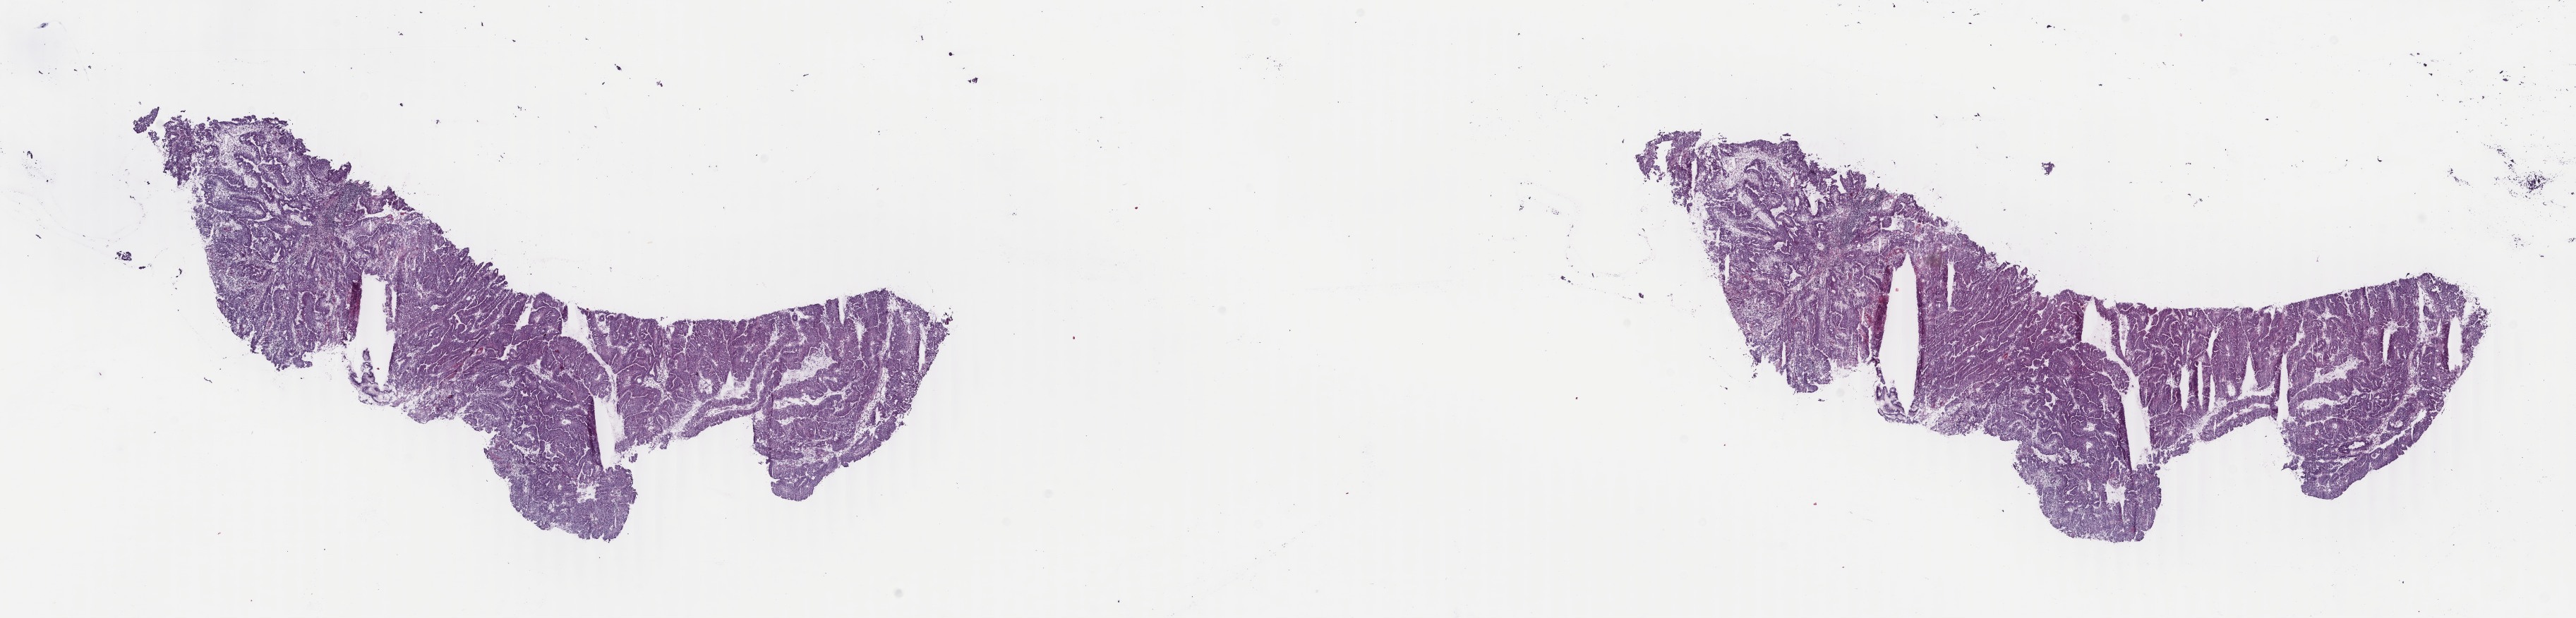
Digitized H&E tissue section (whole slide), low-resolution overview of the scanned area, about 29.0 x 7.0 mm (from a 40x scan). Frozen section from the top of the tissue portion. Sample: primary tumour, stomach. Male patient; age at initial diagnosis 70 years. Composition of this section per pathologist review: tumour cells 100%, tumour nuclei 94%.
Histologic diagnosis: Adenocarcinoma, intestinal type (gastric antrum).